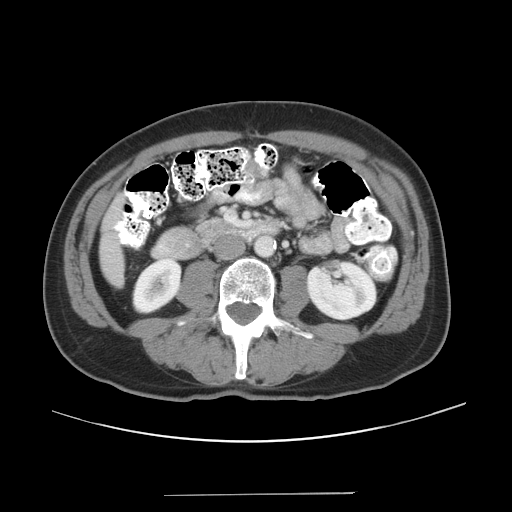
Contrast-enhanced abdominal CT, one axial slice; reconstruction kernel STANDARD; 120 kVp; soft-tissue window (W 400 / L 40 HU); 5 mm slice thickness; 512 × 512 image matrix, field of view 409 × 409 mm. Male patient, age 65 years. Case-level facts recorded for this patient, not image findings: diagnosis: colorectal cancer liver metastases, imaged before liver resection; multiple liver metastases: no; largest metastasis: 3.8 cm; disease in both lobes: no.
Structures marked on this image (manually delineated by an expert):
- liver: bounding box <102,201,123,284> (left, top, right, bottom; pixels)
- planned liver remnant (the part of the liver to remain after resection): <102,201,123,284>